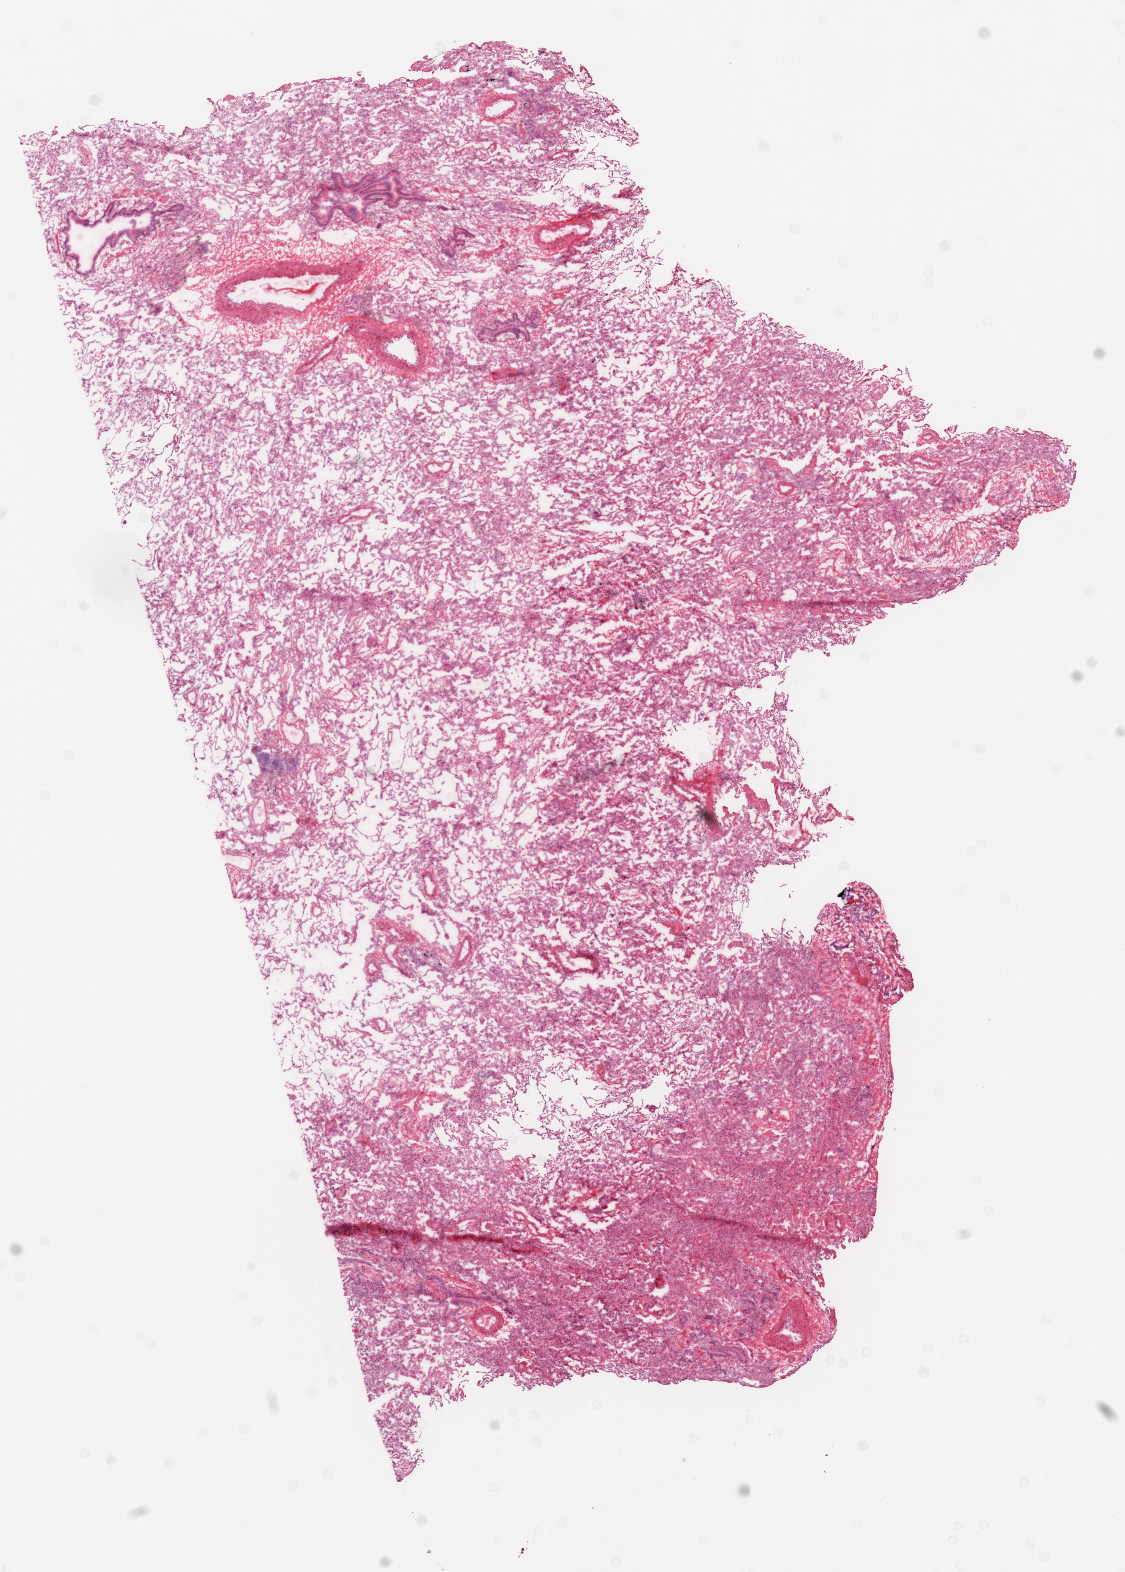
H&E whole-slide image, low-resolution overview of the scanned area, about 9.0 x 12.6 mm (slide scanned at 20x), frozen section from the top of the tissue portion, sample: solid tissue normal (non-tumour tissue), lung. Patient: male, age at initial diagnosis 57 years.
* this section: solid tissue normal sample (biorepository sample class)
* patient diagnosis: Squamous cell carcinoma, NOS (lower lobe, lung)